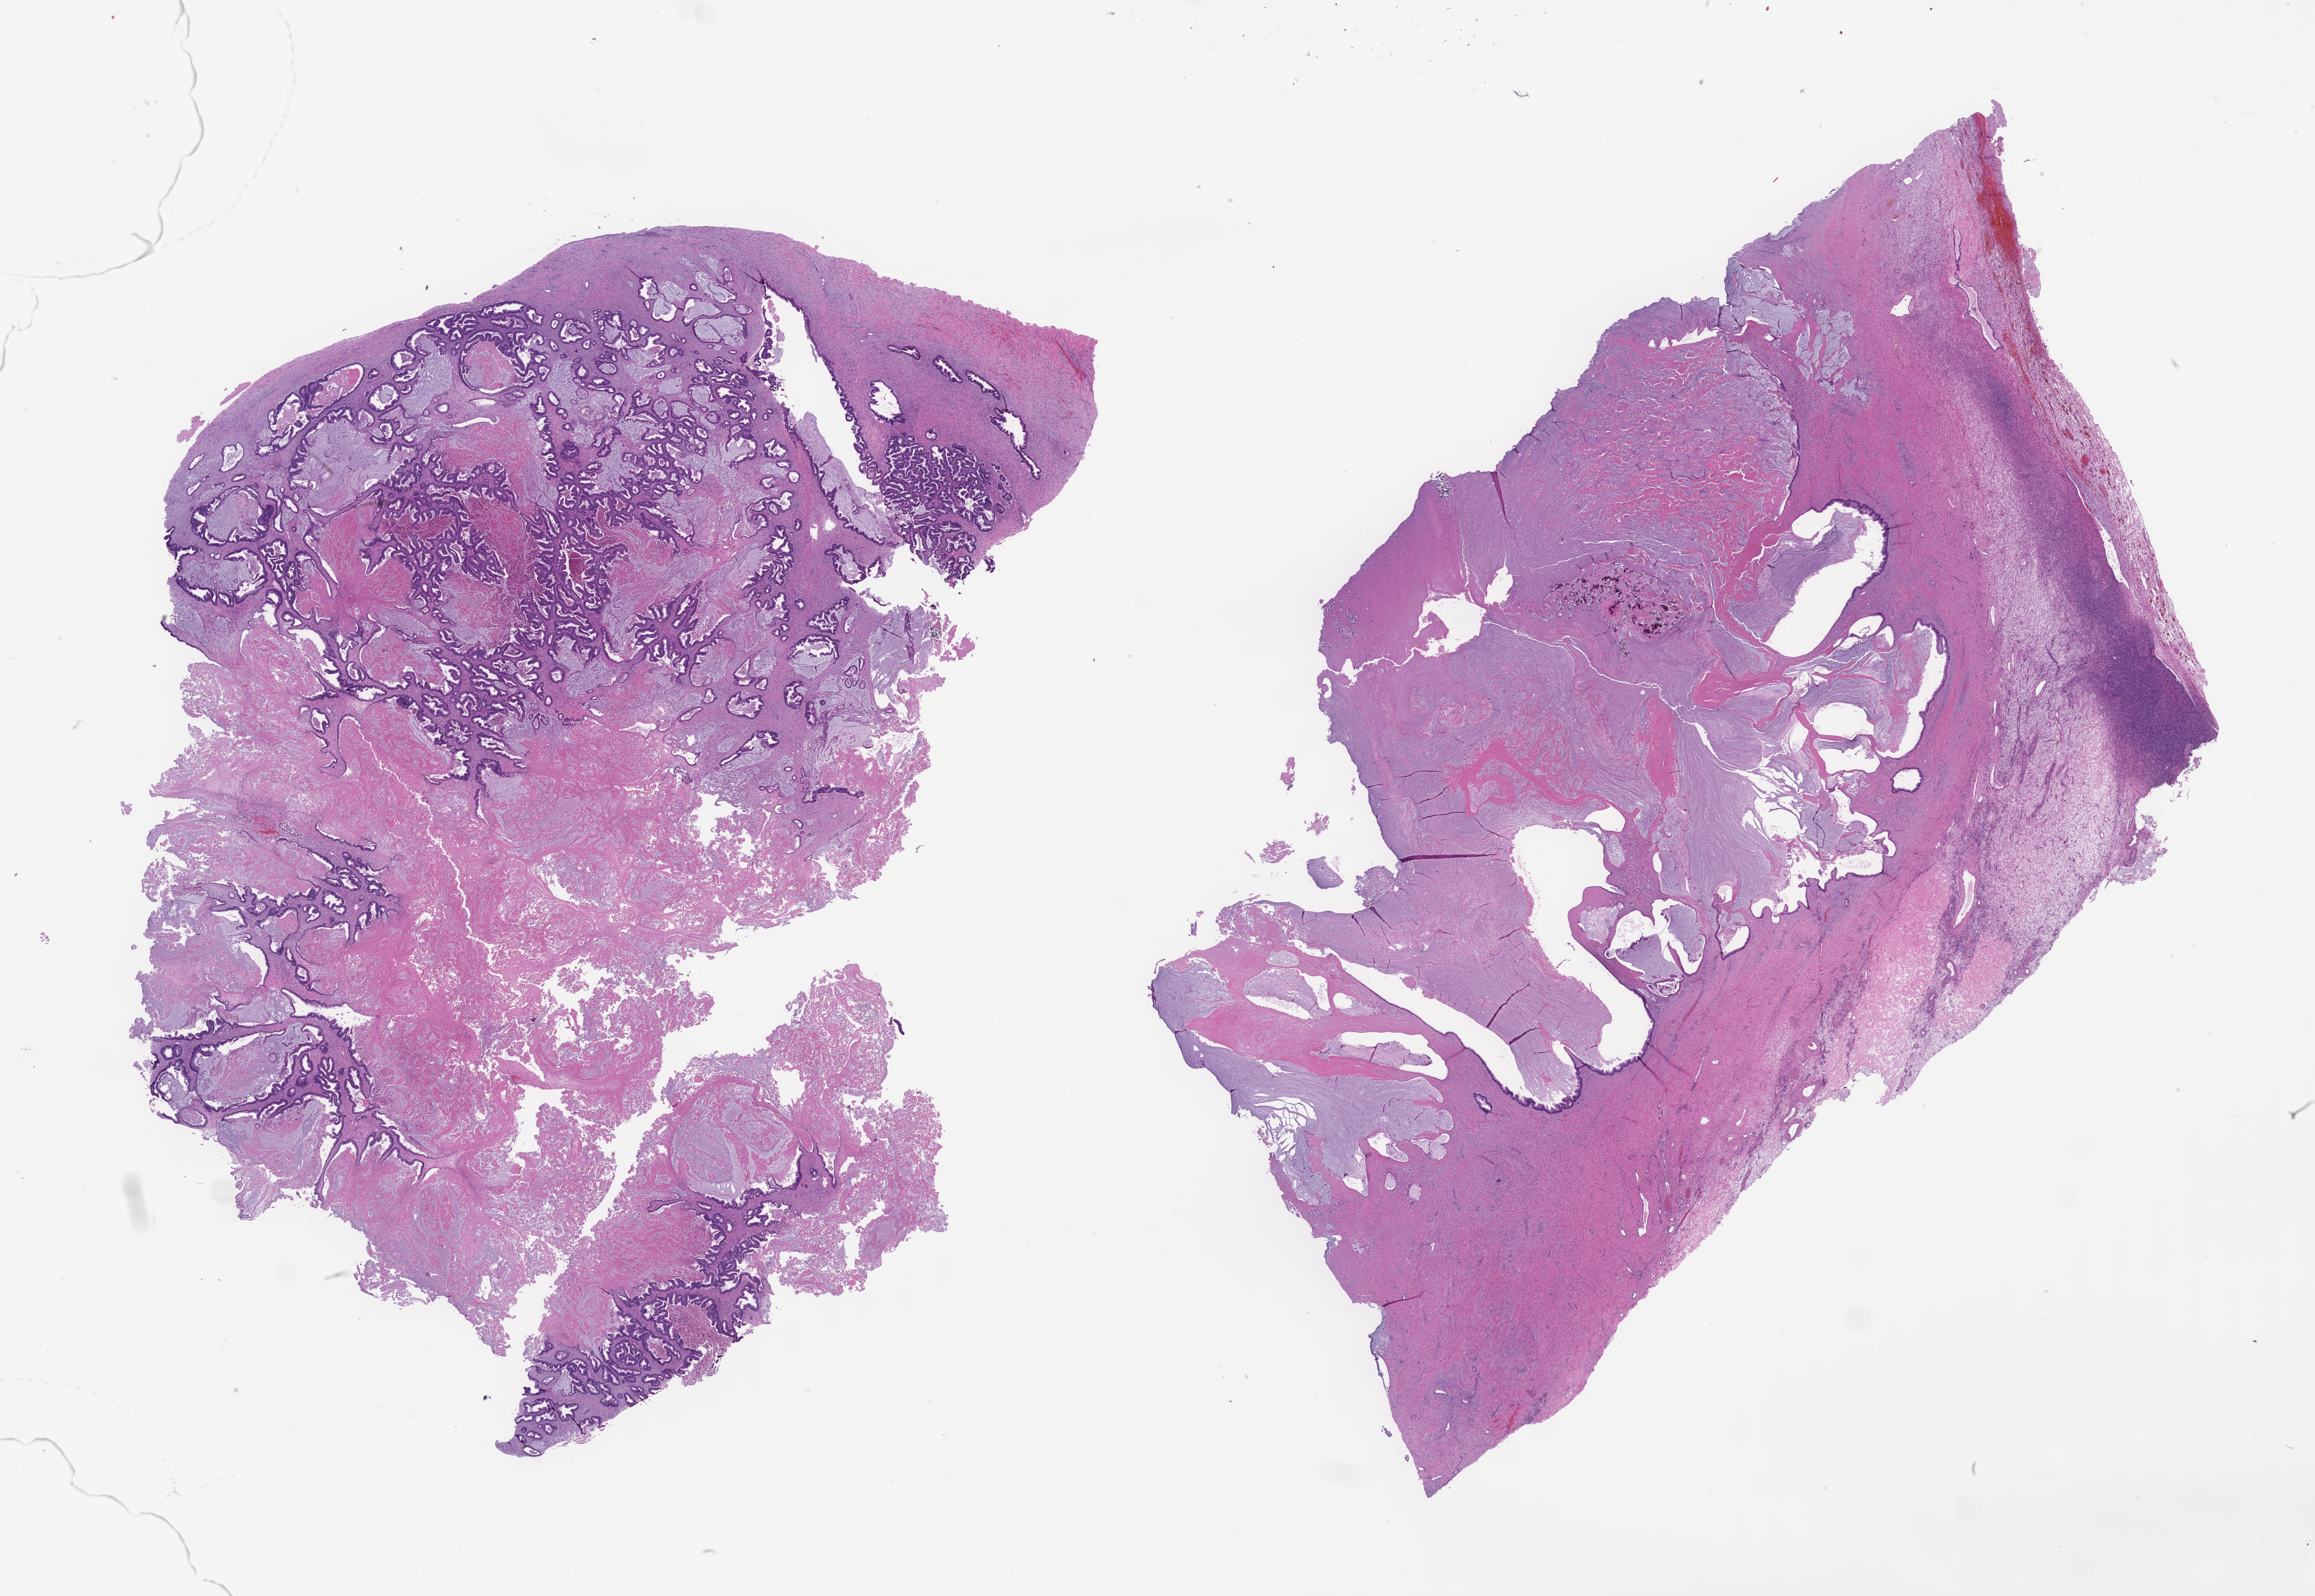
Whole-slide image, H&E stain, low-resolution overview of the scanned area, about 30.7 x 21.1 mm. Formalin-fixed paraffin-embedded section. Specimen time point: archival tissue. Patient: female.
This section: metastasis (sampled organ not recorded). Patient diagnosis (primary): Colorectal Carcinoma.